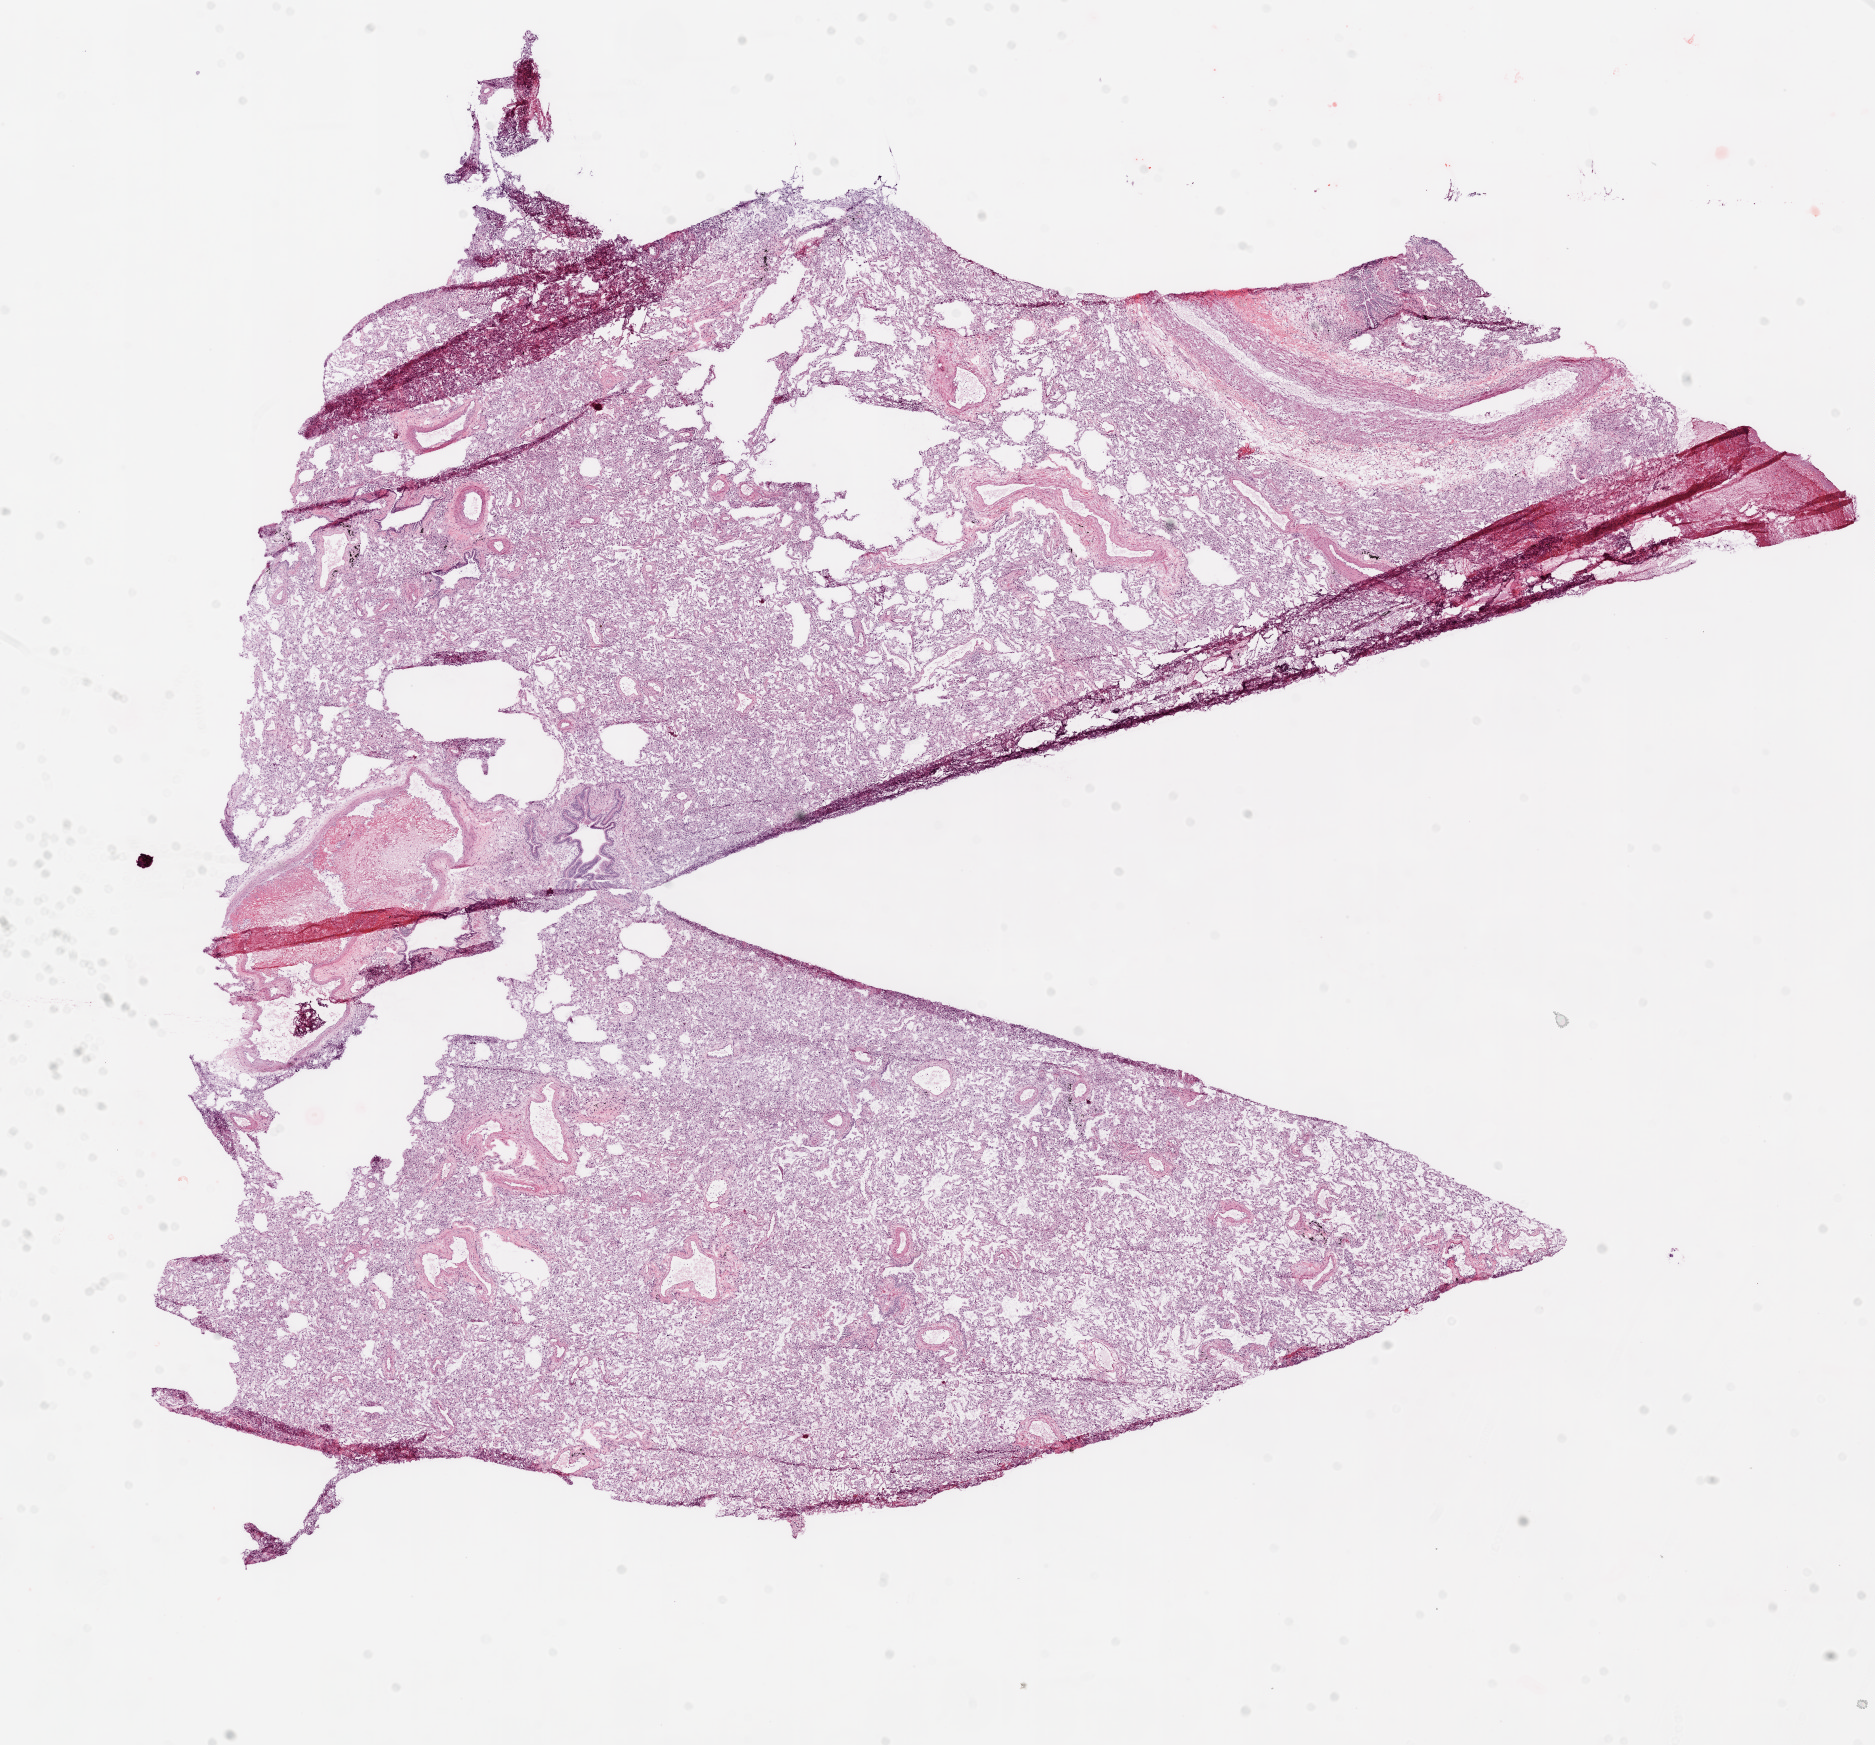
Digitized H&E tissue section (whole slide) — shown as a low-resolution overview of the whole scanned area (about 15.0 x 14.0 mm, slide scanned at 20x); frozen section from the top of the tissue portion; sample: solid tissue normal (non-tumour tissue), lung. Patient: male, age at initial diagnosis 66 years.
This section: solid tissue normal (non-tumour) sample from the same patient. Patient diagnosis: Adenocarcinoma, NOS.